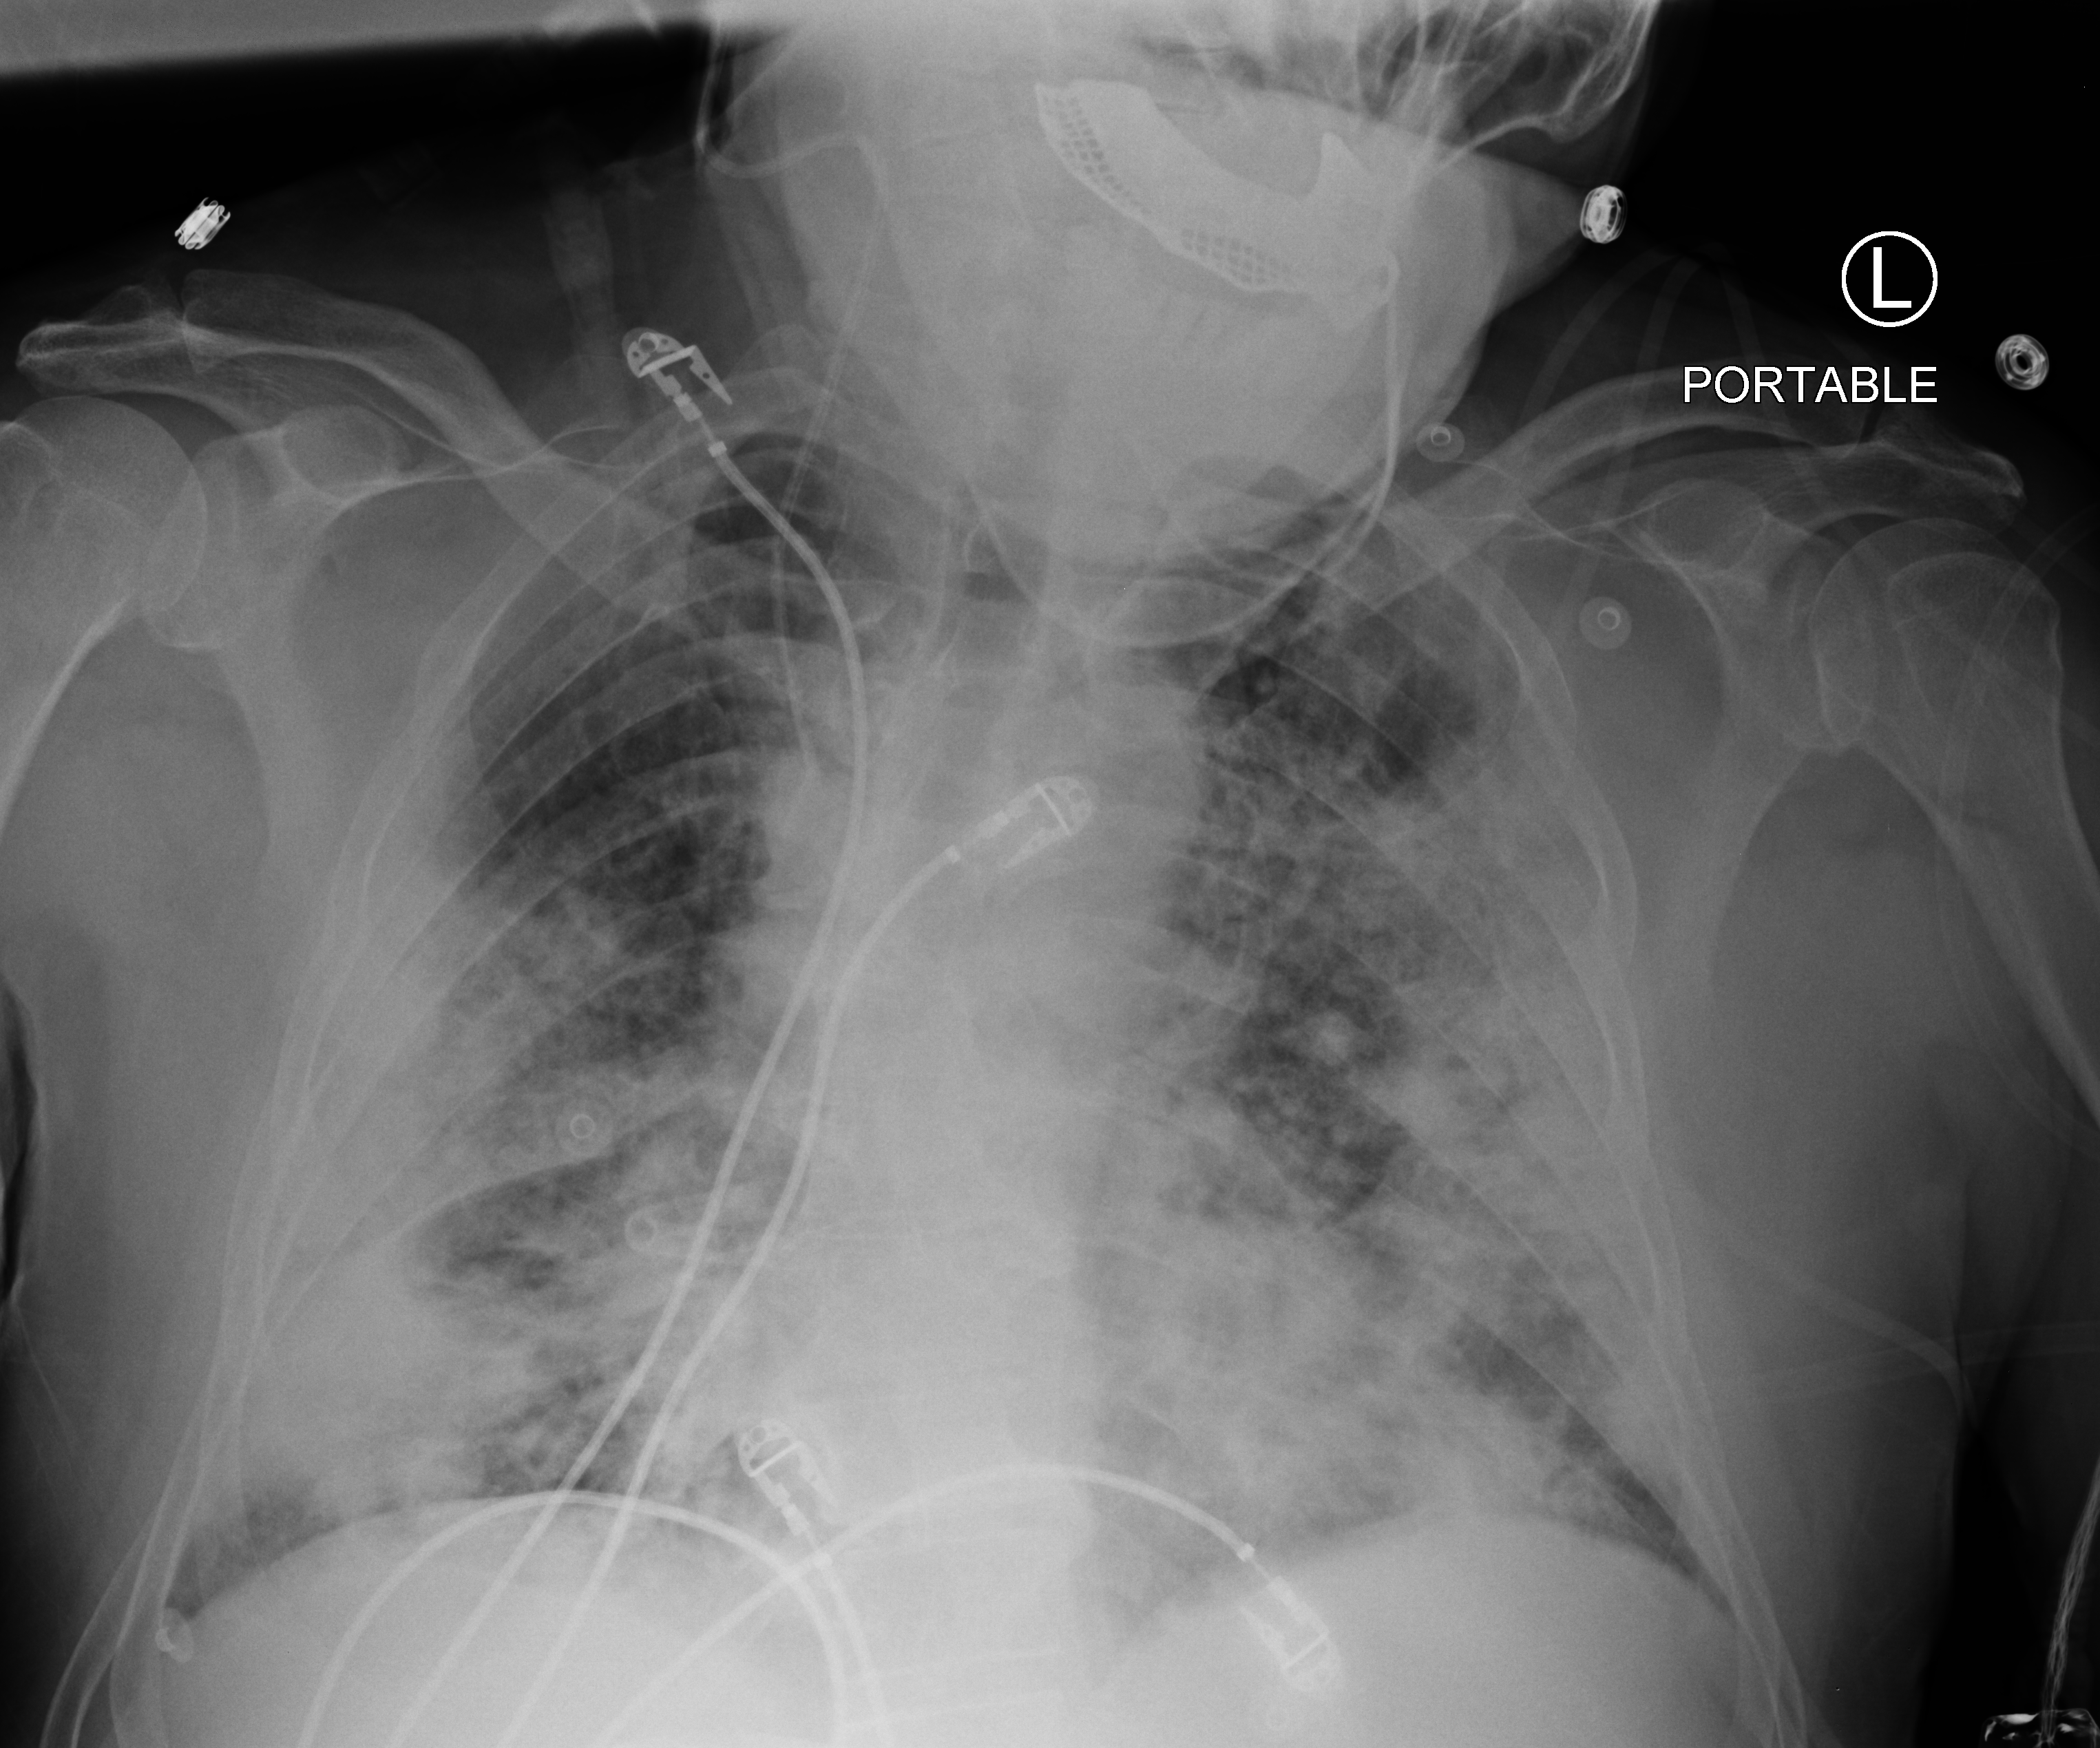
Bedside chest radiograph (computed radiography); anteroposterior (AP) projection. Male patient hospitalised with COVID-19, age 60–74 years.
From the hospital-stay record, not from the radiograph (when in the stay this image was taken is not recorded): smoking status (admission record): never; mechanically ventilated during this hospital stay: yes; length of hospital stay: 32 days.